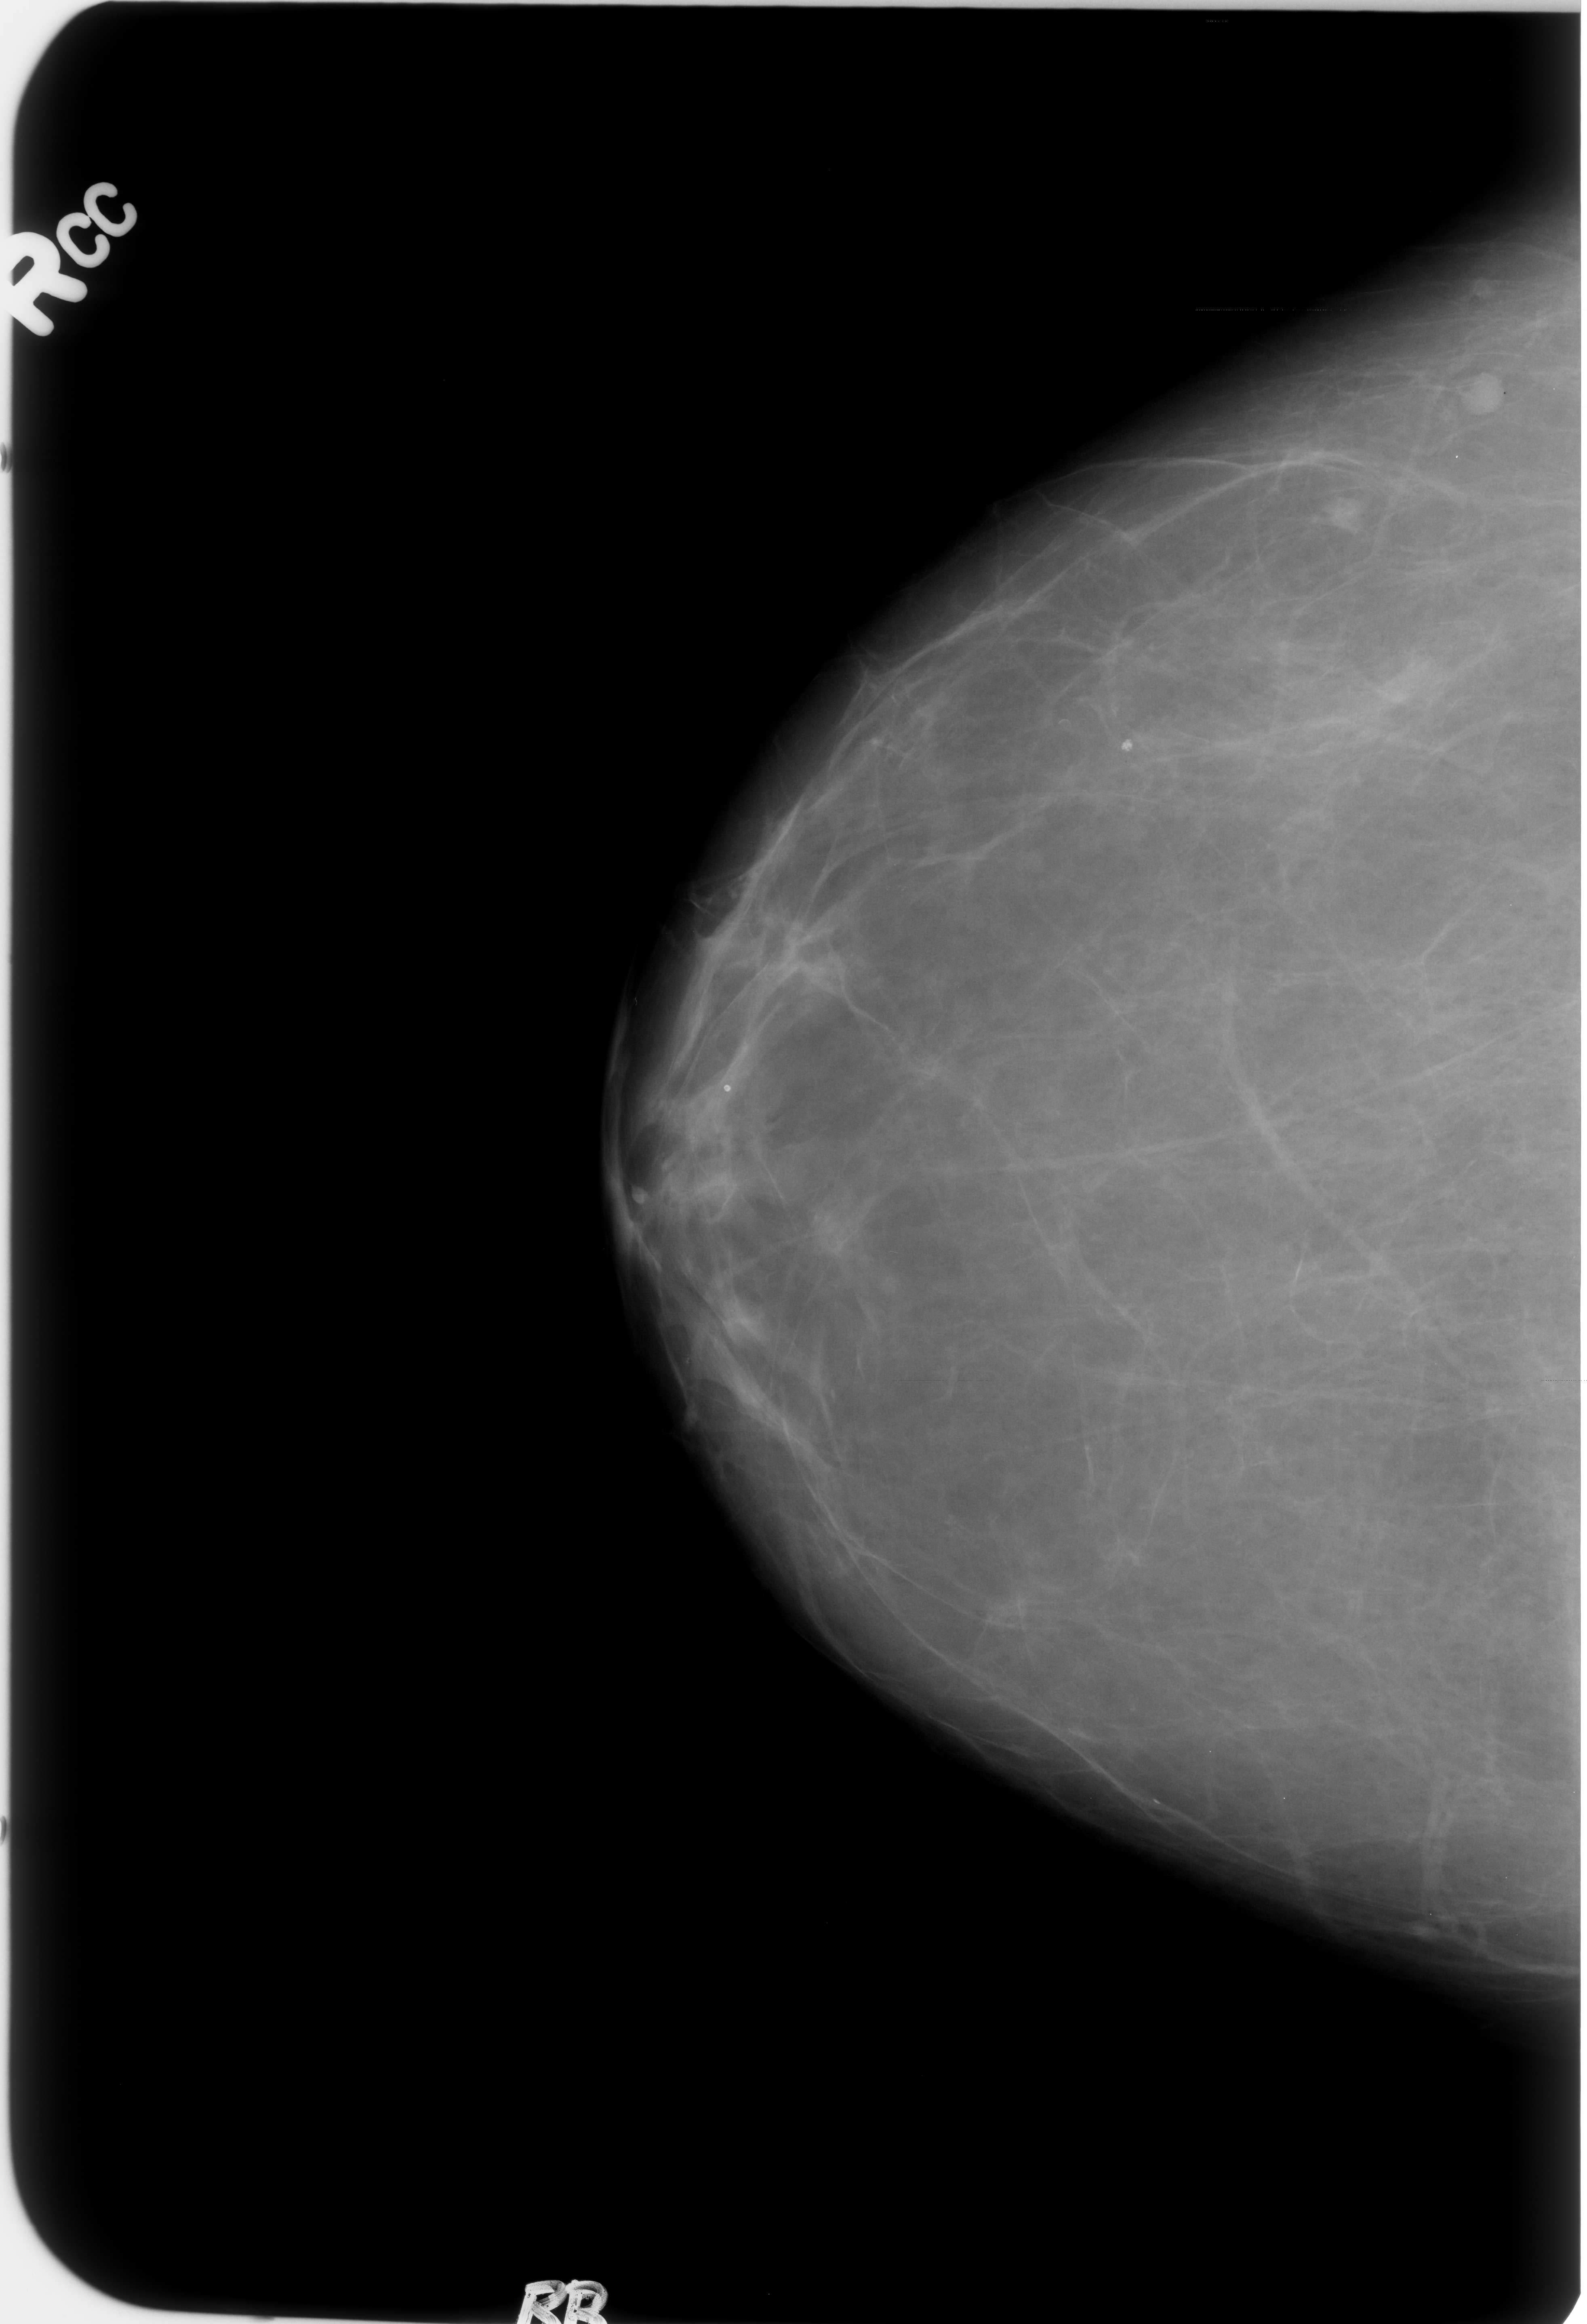
Mammogram (digitized film). Right breast. Craniocaudal (CC) view. BI-RADS breast density category 1 (scale 1–4). 1587 × 2324 image matrix.
Expert-marked regions of interest on this image (one box per marked abnormality):
- calcifications, morphology coarse; BI-RADS assessment category 2; benign; no additional work-up was recommended (outcome (as recorded, no biopsy): benign without callback): bounding box [x1, y1, x2, y2] px = [707, 1073, 751, 1106]